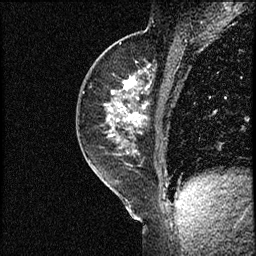
Breast MRI (dynamic contrast-enhanced), one sagittal slice. Position 32 of 56 along the scan axis. Dynamic contrast-enhanced study with each time point stored as its own series, time point 2 of 3 at this slice position (early post-contrast, ordered by acquisition time). 1.5 T. TE 4.2 ms, TR 17.3 ms. 2 mm slice thickness. 256 × 256 image matrix, field of view 200 × 200 mm. Female patient. From the clinical record (not read from this slice): setting: breast cancer imaged before/during neoadjuvant chemotherapy; receptor status: HER2-positive.
Annotated regions visible in this slice (semi-automatic segmentation, software-assisted and operator-edited):
- analysis volume of interest (the breast-tissue region the enhancement analysis was run in; not a lesion): bounding box [x1, y1, x2, y2] px = [76, 50, 156, 155]
- tumour enhancement mask (voxels above the 100 % enhancement threshold inside the analysis volume of interest): [106, 77, 150, 136]